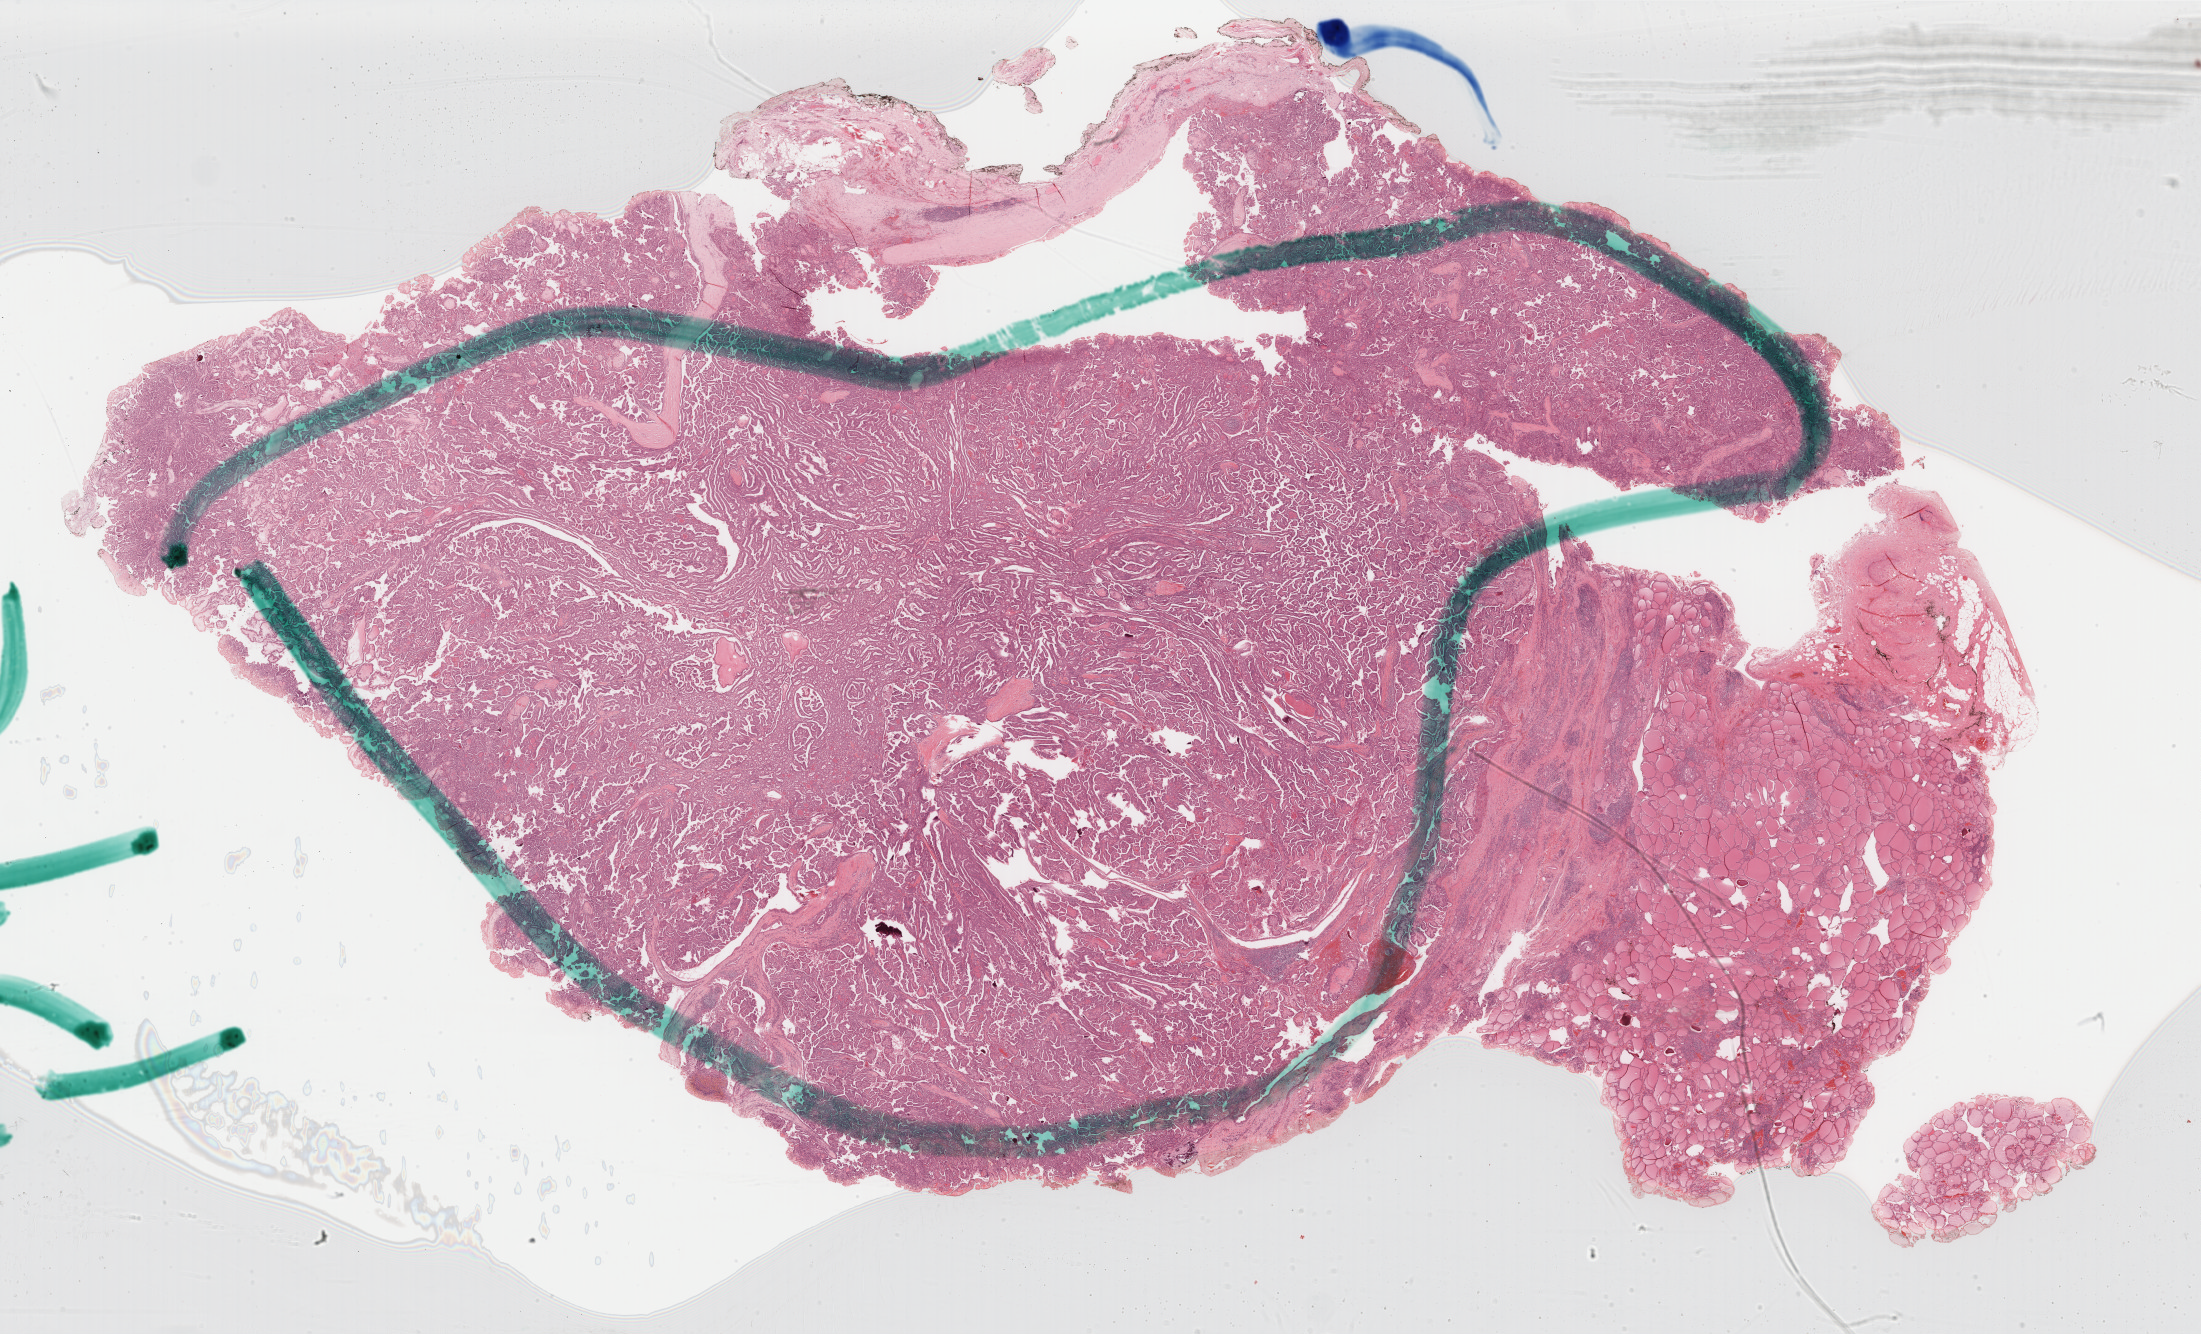
Digitized H&E-stained tissue section (whole slide) — a low-resolution overview of the entire scanned area, about 34.9 x 21.2 mm, FFPE section, sample: primary tumour, thyroid. Female patient; age at initial diagnosis 28 years.
- diagnosis: Papillary adenocarcinoma, NOS (thyroid gland)
- laterality: left
- lymph nodes positive (case pathology): 2 of 2 examined
- AJCC pathologic stage: I